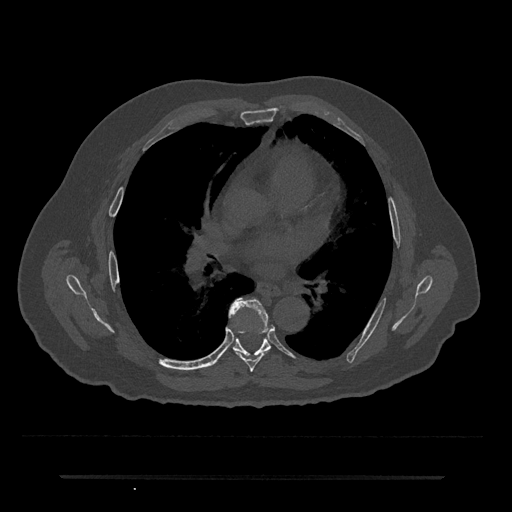
CT including the spine, one axial slice; position 413 of 797 along the scan axis; reconstruction kernel Br40s/3; 120 kVp; bone window (W 1800 / L 400 HU); 0.5 mm slice thickness; 512 × 512 image matrix, field of view 437 × 437 mm. Male patient, age 69 years. From the clinical record (not read from this slice): primary cancer: prostate.
Annotated regions visible in this slice (semi-automatically segmented with operator editing):
- T6 vertebra: bounding box <230,298,272,372> (left, top, right, bottom; pixels)
- T7 vertebra: <216,338,271,364>